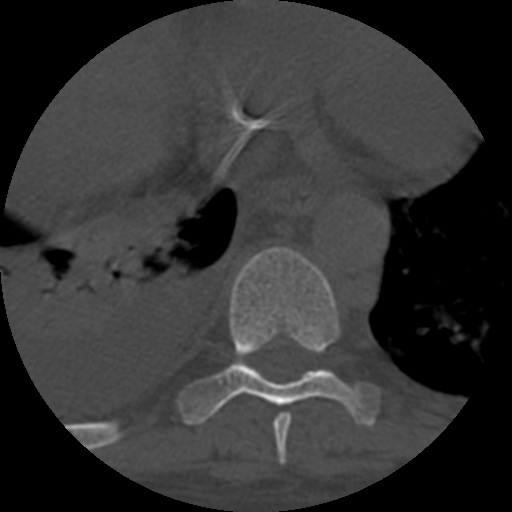
CT including the spine, one axial slice; position 378 of 708 along the scan axis; reconstruction kernel STANDARD; 120 kVp; one of 3 acquisitions stored at this slice position; bone window (W 1800 / L 400 HU); 512 × 512 image matrix. Patient age 55 years. Case-level facts recorded for this patient, not image findings: primary cancer: colon; vertebrae with lytic lesions (as recorded): T12, L1, L5.
Annotated regions visible in this slice (semi-automatically segmented with operator editing):
- T8 vertebra: box from (x=273, y=413) to (x=292, y=464) px
- T9 vertebra: (x=174, y=247)–(x=380, y=426)